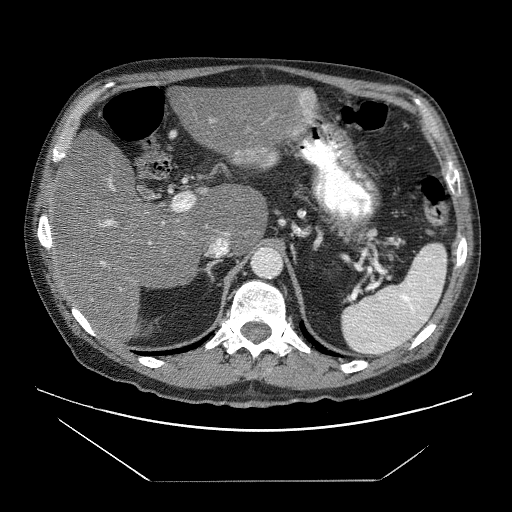
Contrast-enhanced abdominal CT (liver protocol), one axial slice. Position 39 of 83 along the scan axis. Reconstruction kernel STANDARD. 120 kVp. Soft-tissue window (W 400 / L 40 HU). 512 × 512 image matrix, field of view 420 × 420 mm. From the clinical record (not read from this slice): diagnosis: hepatocellular carcinoma (patient treated with transarterial chemoembolisation; whether this scan precedes or follows treatment is not stated here); TNM stage (as recorded): Stage-IVB; Child-Pugh class: B.
Outlined on this slice (semi-automatic segmentation, software-assisted and operator-edited):
- liver parenchyma outside the tumour (the mass and vessels are separate outlines, so this box may not span the whole liver): bounding box [x1, y1, x2, y2] px = [52, 86, 312, 342]
- mass: [232, 89, 317, 166]
- liver vessels: [98, 131, 297, 266]